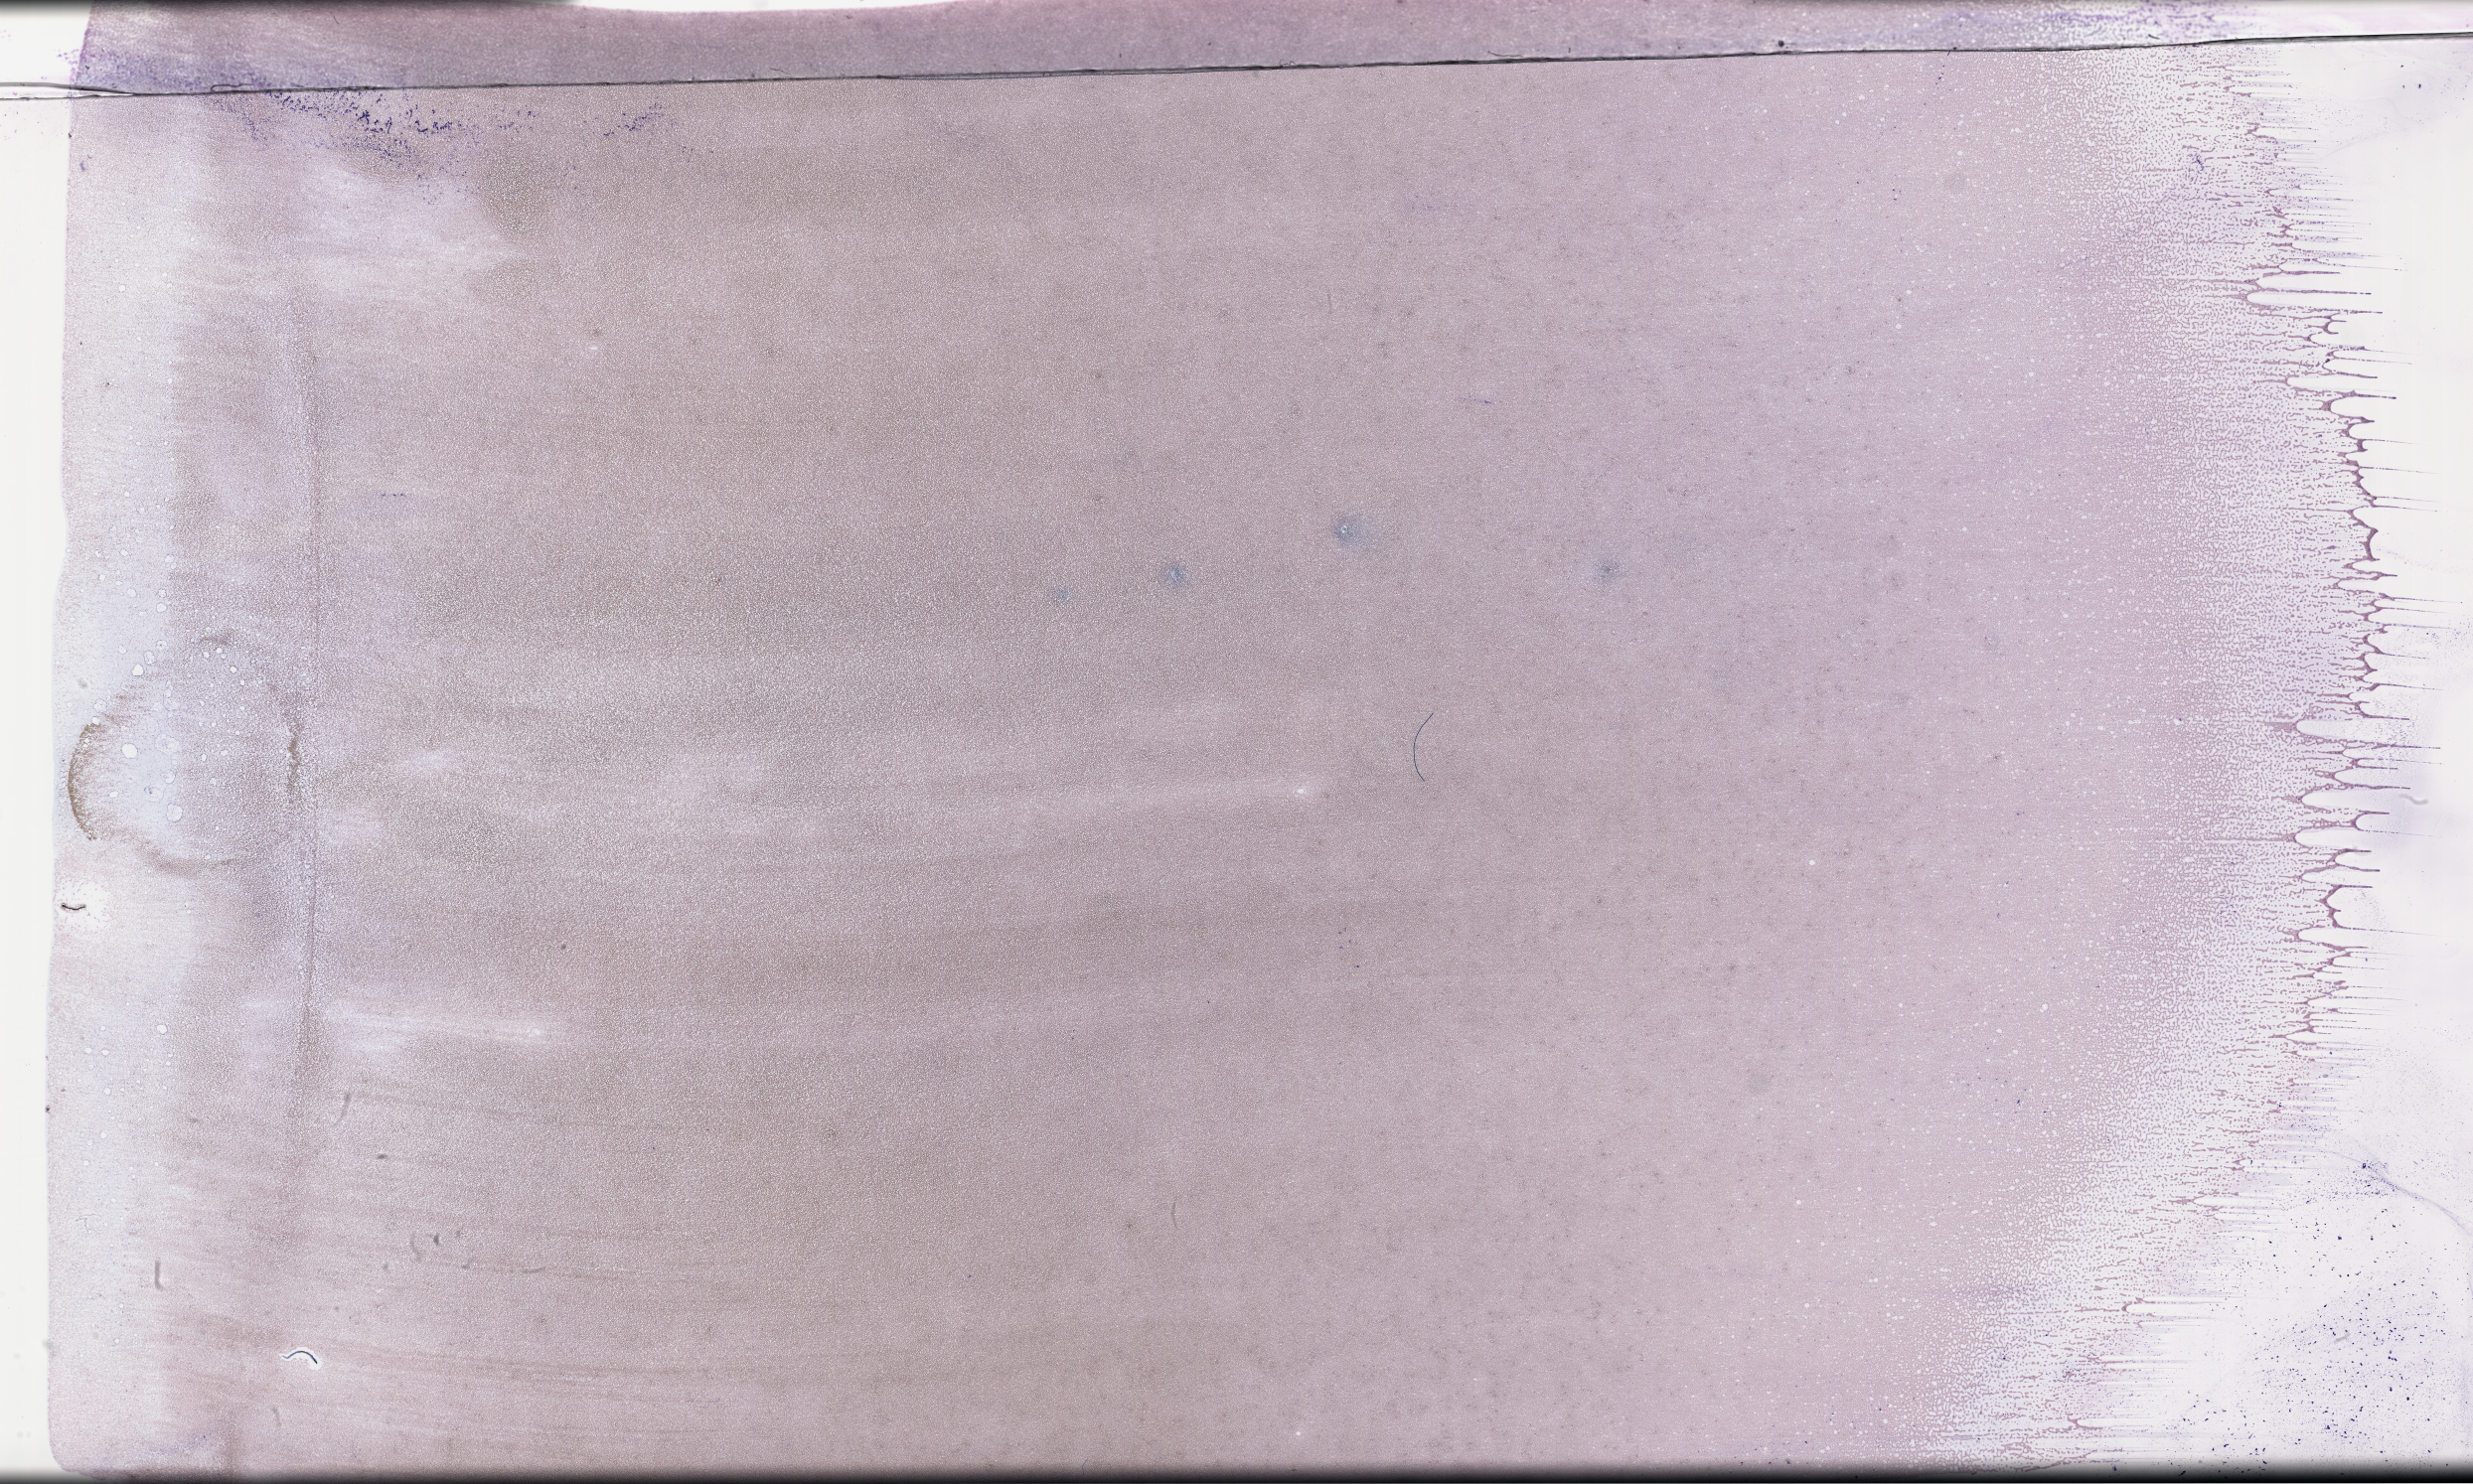
Whole-slide image of a whole blood smear, Wright-Giemsa stain — whole scanned area (about 40.2 x 24.1 mm) shown as a low-resolution overview, smear from an EDTA sample, specimen time point: collected on treatment. Male patient.
From a patient with: Plasma Cell Myeloma.